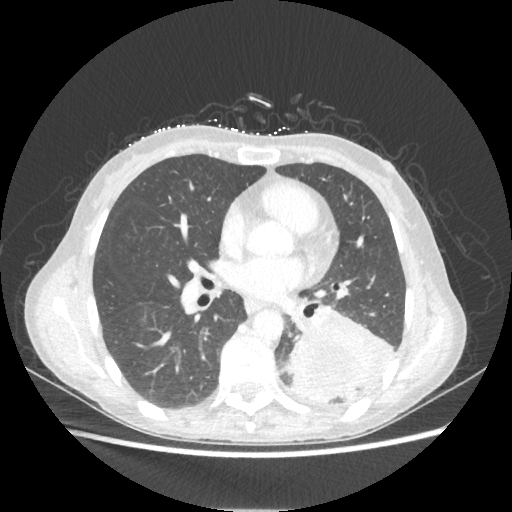
Chest CT, one axial slice; position 111 of 221 along the scan axis; reconstruction kernel STANDARD; lung window (W 1500 / L -600 HU); 512 × 512 image matrix, field of view 360 × 360 mm. Patient: female, 53 years. From the clinical record (not read from this slice): clinical TNM (as recorded): T3 N0 M0.
Structures marked on this image (rectangle marked by the reading radiologist):
- lung tumour (recorded histology: adenocarcinoma): bounding box <287,307,398,403> (left, top, right, bottom; pixels)